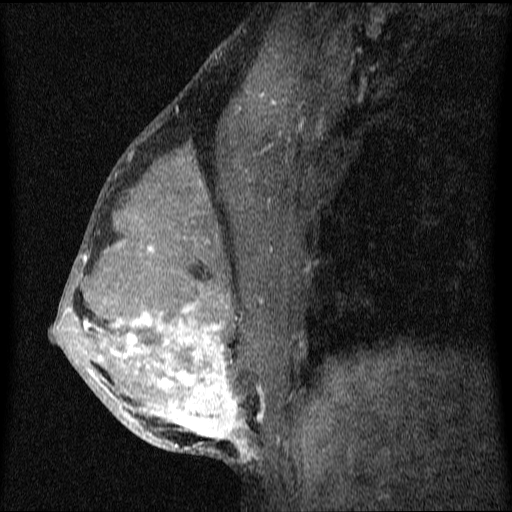
Breast MRI (dynamic contrast-enhanced), one sagittal slice; position 37 of 64 along the scan axis; dynamic contrast-enhanced series, image 2 of 4 at this slice position (ordered by acquisition); 1.5 T; TE 4.2 ms, TR 9.1 ms; 2 mm slice thickness; 512 × 512 image matrix. Female patient, age 33 years.
Structures marked on this image (semi-automatically segmented with operator editing):
- analysis volume of interest (the breast-tissue region the enhancement analysis was run in; not a lesion): bounding box (x1, y1, x2, y2) in pixels: (53, 151, 336, 458)
- tumour enhancement mask (voxels above the 70 % enhancement threshold inside the analysis volume of interest): (53, 241, 254, 458)